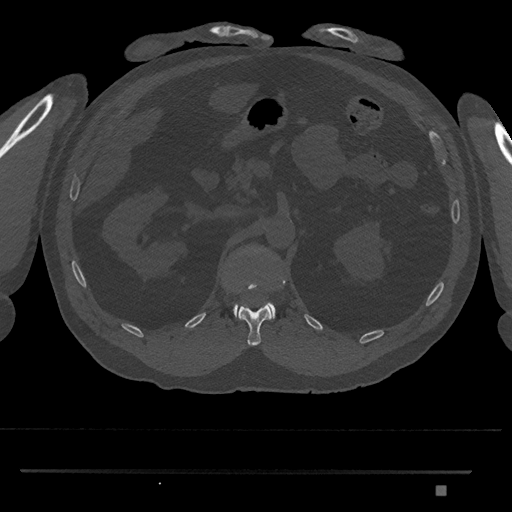
CT including the spine, one axial slice. Slice 863 of 1134 in the series (ordered by position). Bone window (W 1800 / L 400 HU). 0.5 mm slice thickness. 512 × 512 image matrix, field of view 429 × 429 mm. Patient: male, 65 years. From the clinical record (not read from this slice): primary cancer: prostate.
Structures marked on this image (semi-automatically segmented with operator editing):
- L1 vertebra: bounding box (x1, y1, x2, y2) in pixels: (233, 245, 276, 319)
- T12 vertebra: (237, 280, 284, 346)